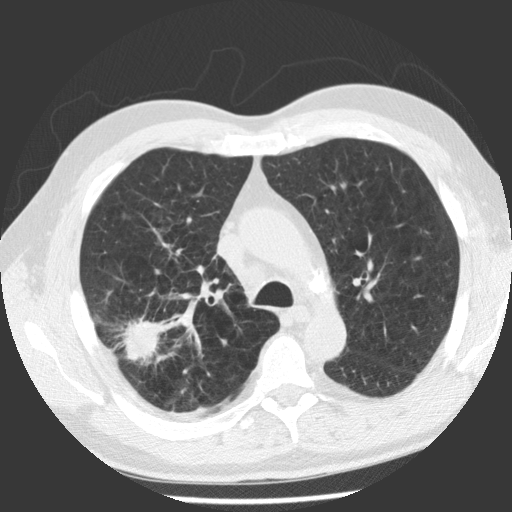
Low-dose screening chest CT, one axial slice. Slice 77 of 112 in the series (ordered by position). Lung window (W 1500 / L -600 HU). 512 × 512 image matrix, field of view 344 × 344 mm.
Annotated regions visible in this slice (outlined manually by an expert reader):
- lesion 1 (tumor, upper lobe of right lung): bounding box [x1, y1, x2, y2] px = [121, 317, 162, 361]